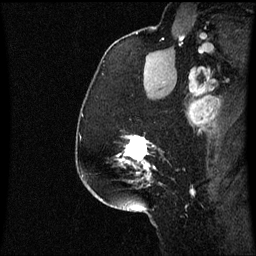
Breast MRI (dynamic contrast-enhanced), one sagittal slice; slice 45 of 60 in the series (ordered by position); dynamic contrast-enhanced series, image 2 of 3 at this slice position (ordered by acquisition); 1.5 T; TE 4.2 ms, TR 8.9 ms; 2 mm slice thickness; 256 × 256 image matrix. Female patient, age 58 years. From the clinical record (not read from this slice): setting: breast cancer imaged before/during neoadjuvant chemotherapy; receptor status: triple-negative.
Outlined on this slice (semi-automatic segmentation, software-assisted and operator-edited):
- analysis volume of interest (the breast-tissue region the enhancement analysis was run in; not a lesion): bounding box <116,136,157,179> (left, top, right, bottom; pixels)
- tumour enhancement mask (voxels above the 70 % enhancement threshold inside the analysis volume of interest): <122,136,155,179>